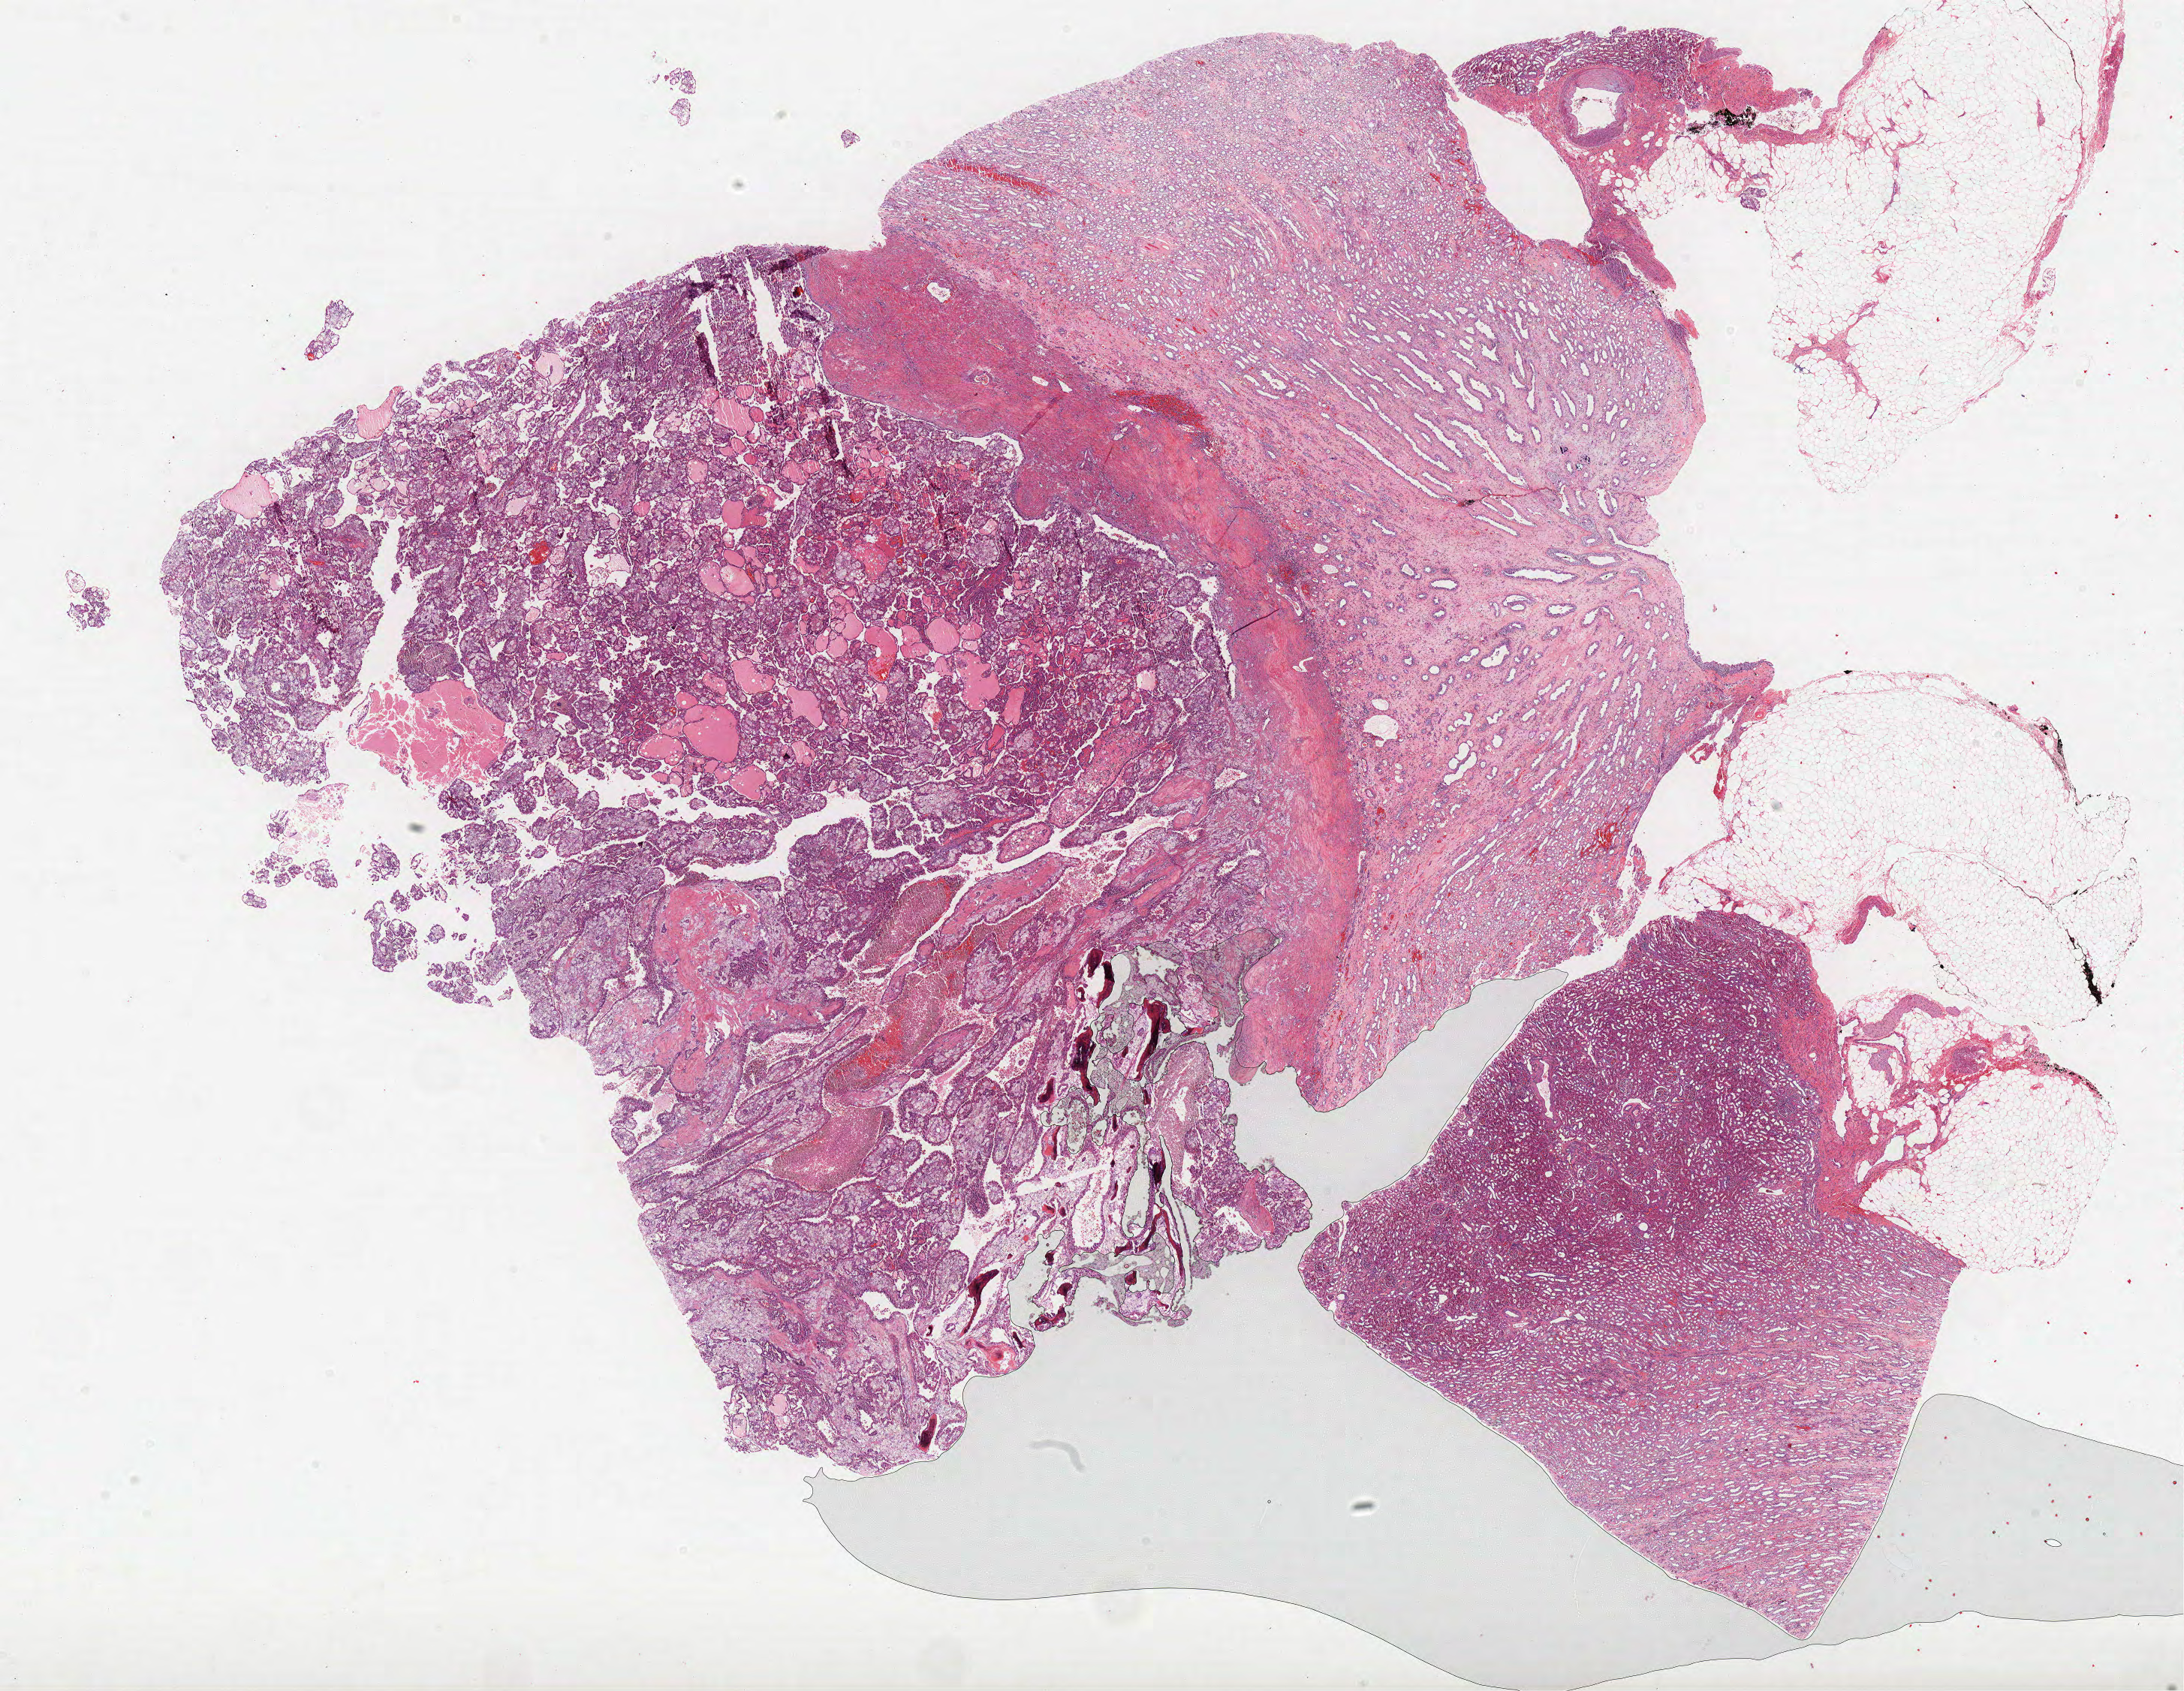
Digitized H&E-stained tissue section (whole slide), a low-resolution overview of the entire scanned area, about 23.3 x 18.0 mm, FFPE section, primary tumour sample from the kidney. Male patient; age at initial diagnosis 61 years.
Histologic diagnosis: Papillary adenocarcinoma, NOS. AJCC pathologic stage: I. Laterality: left.